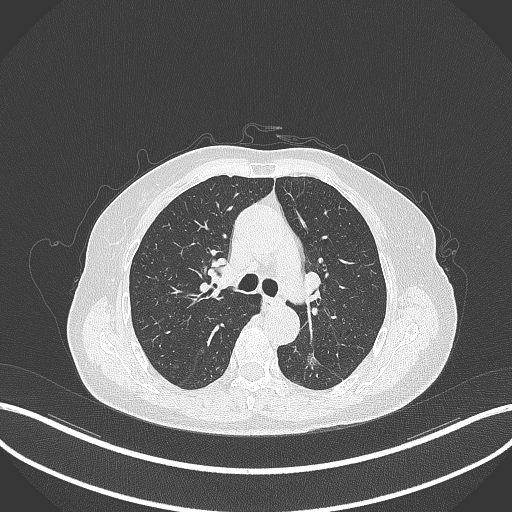
Chest CT, one axial slice; slice 198 of 352 in the series (ordered by position); reconstruction kernel B70f; 120 kVp; lung window (W 1500 / L -600 HU); 1 mm slice thickness; 512 × 512 image matrix, field of view 400 × 400 mm. Patient: female, 70 years. From the clinical record (not read from this slice): clinical TNM (as recorded): T1c N0 M0.
Annotated regions visible in this slice (bounding box drawn by a radiologist):
- lung tumour (recorded histology: adenocarcinoma): bounding box [x1, y1, x2, y2] px = [301, 343, 326, 376]